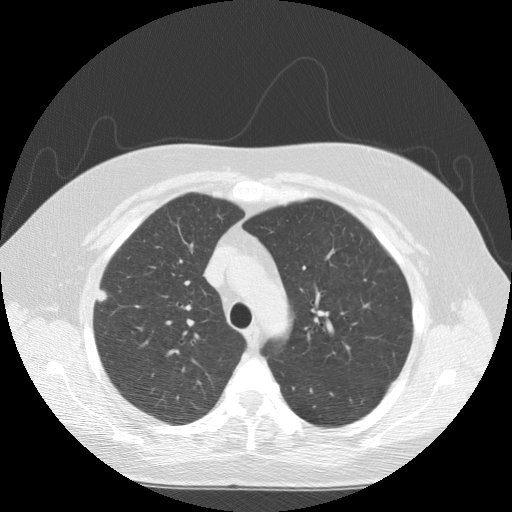
Low-dose screening chest CT, axial slice; first (baseline) screen; lung window (W 1500 / L -600 HU); standard (soft-tissue) reconstruction kernel (STANDARD); slice 37 of 146 in the series. Female participant, aged 55 years at enrolment. Current smoker at enrolment.
Lesion marked by an expert reader, bounding box [x1, y1, x2, y2] px = [84, 281, 121, 318]. The exam's reader record, not a measurement of the box and not confirmed to be the same lesion: non-calcified nodule or mass ≥4 mm, right upper lobe, 8 × 7 mm, spiculated (stellate) margins, soft tissue attenuation. Later outcome: lung cancer diagnosed 98 days after this screen — squamous cell carcinoma, NOS, right upper lobe, poorly differentiated (G3), stage IA (AJCC 6th edition), 8 mm at pathology.